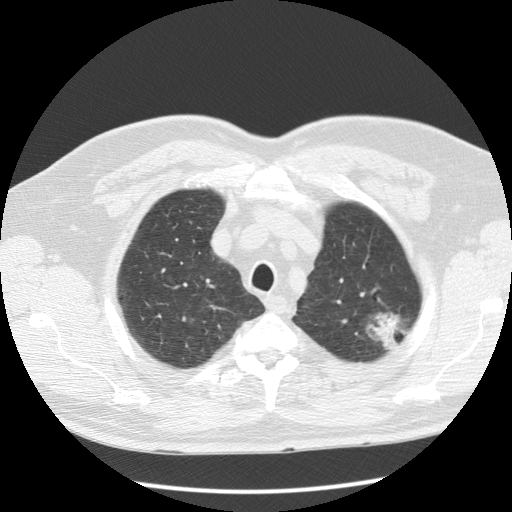
Low-dose screening chest CT, axial slice, first (baseline) screen, lung window (W 1500 / L -600 HU), standard (soft-tissue) reconstruction kernel (STANDARD). Male participant, aged 60 years at enrolment.
Expert reader's lesion annotation, bounding box (x1, y1, x2, y2) in pixels: (354, 297, 415, 358). The screening reader recorded 3 non-calcified nodules or masses ≥4 mm on this exam (left upper lobe, right upper lobe, left upper lobe); which of them this box marks is not recorded. Participant outcome: lung cancer diagnosed 48 days after this screen — bronchiolo-alveolar adenocarcinoma, NOS, left upper lobe, well differentiated (G1), stage IA (AJCC 6th edition), 27 mm at pathology.